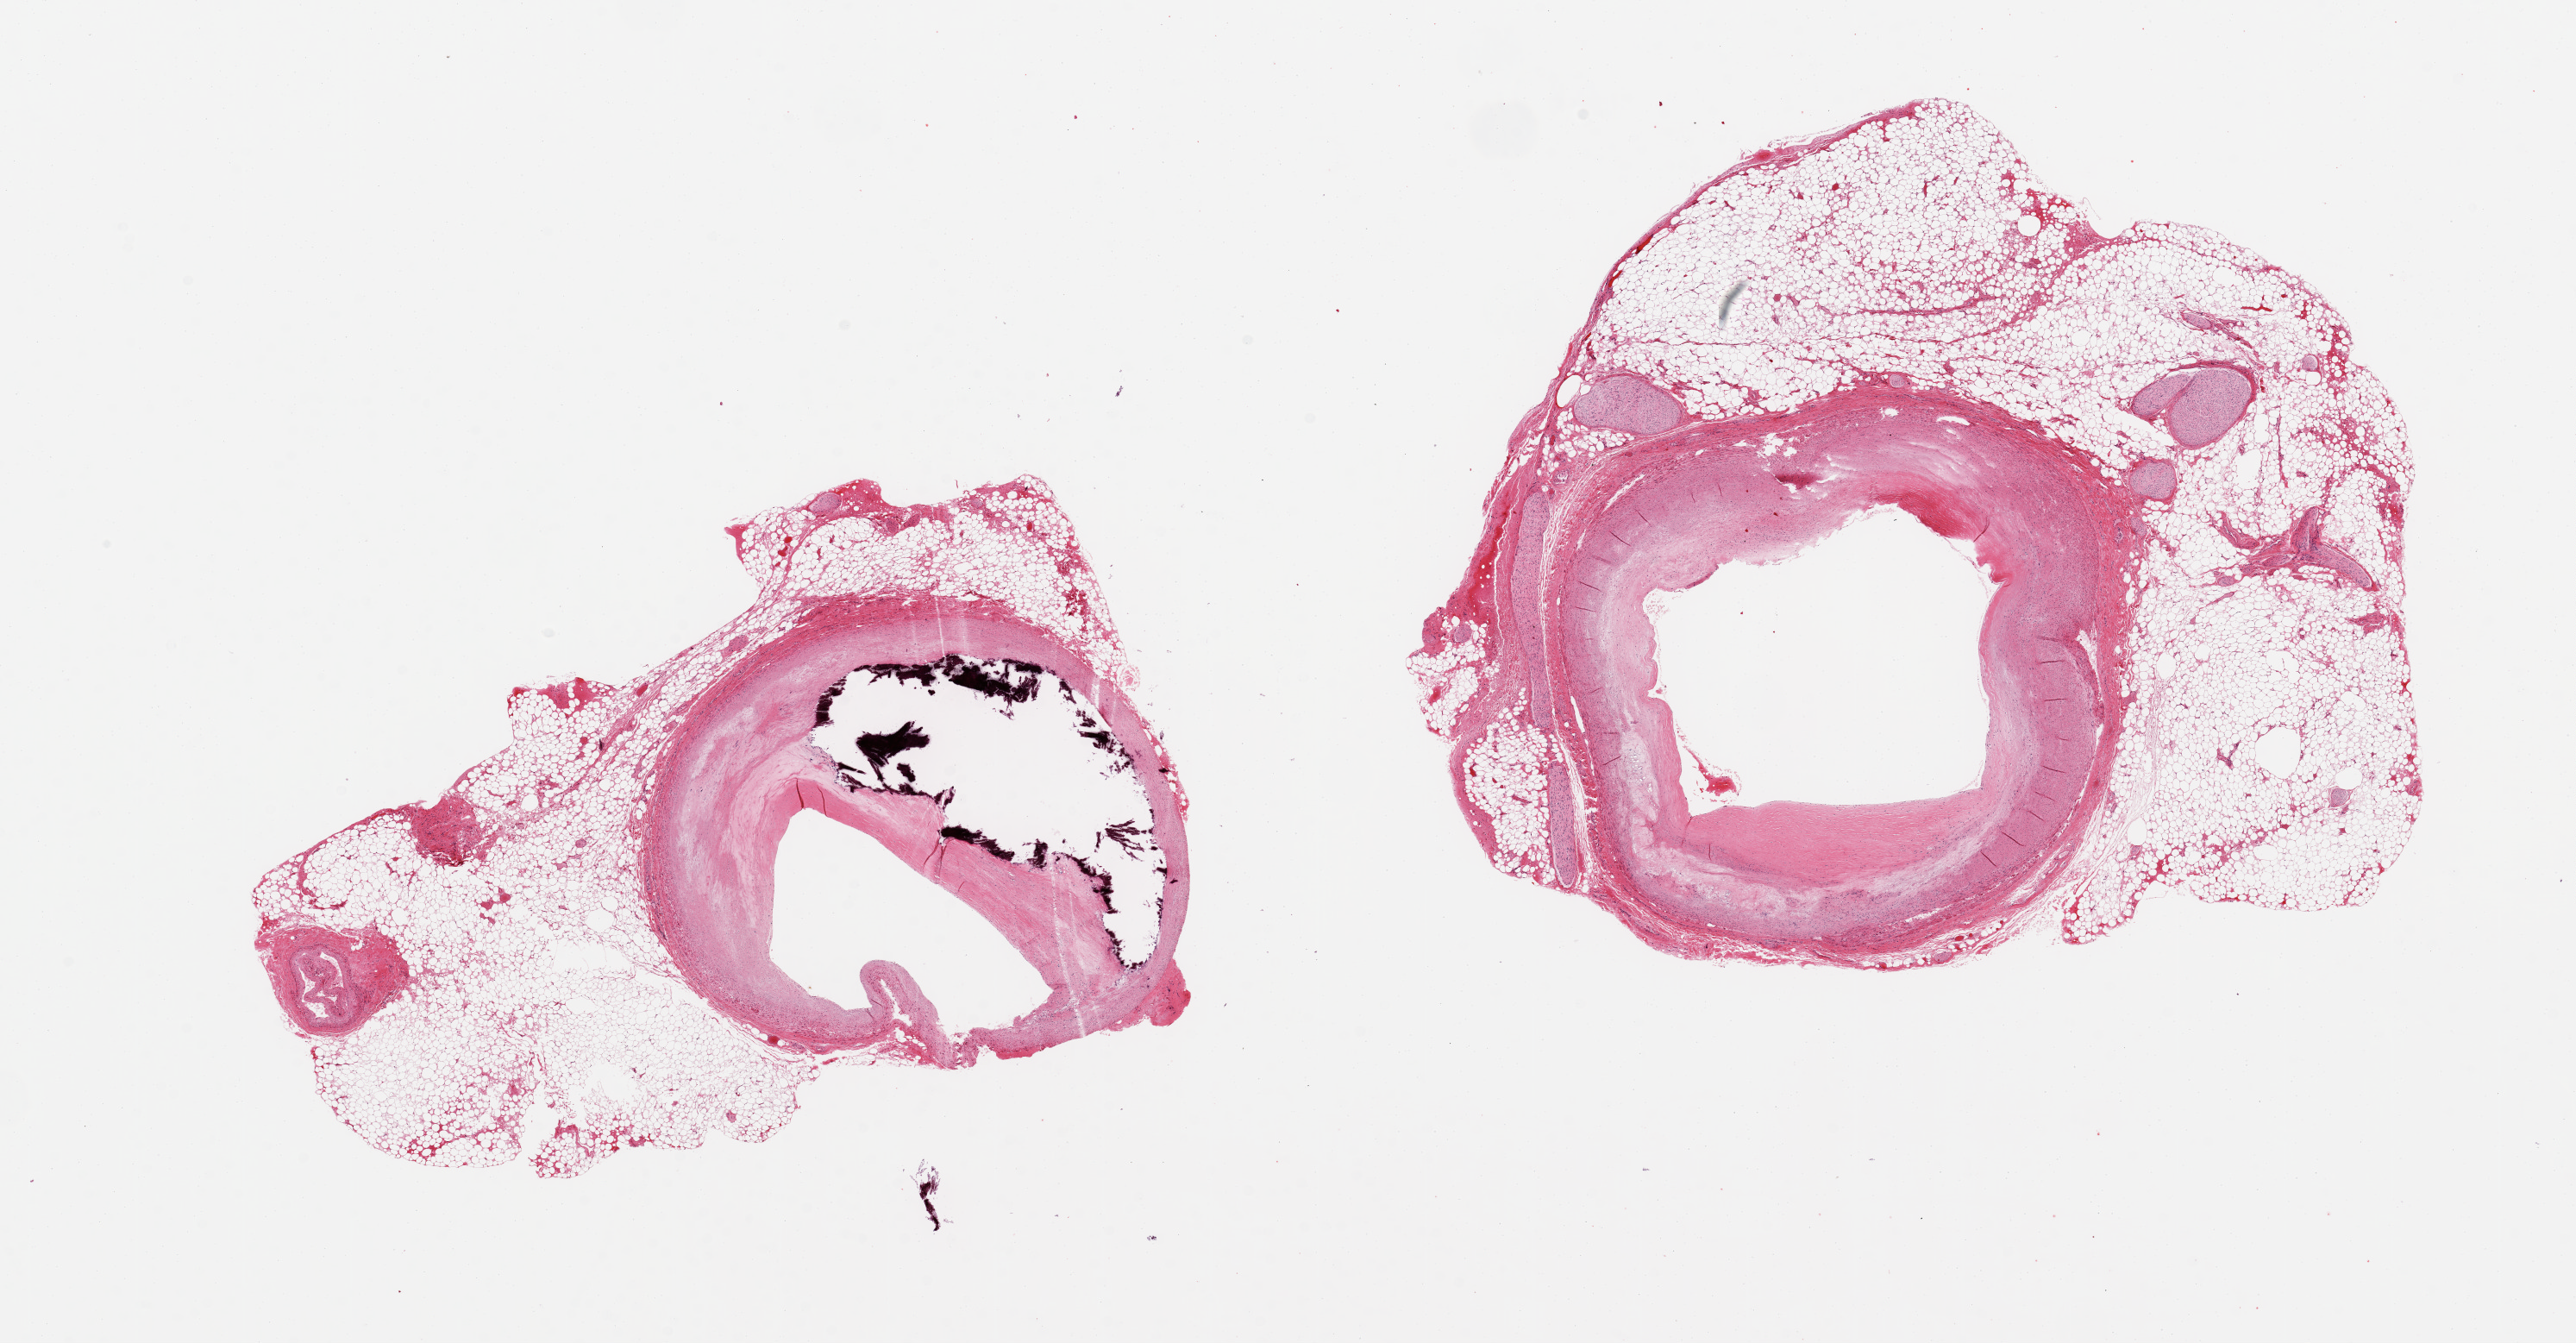
Digitized haematoxylin and eosin-stained section, brightfield, whole scanned area (about 23.6 x 12.3 mm, from a 20x scan) shown as a low-resolution overview, PAXgene-fixed, paraffin-embedded tissue, target tissue: coronary artery, tissue donor sample. Donor sex: male.
• reviewer comment on this tissue sample: 2 pieces ~ 5 mm diameter; 1 with 50% calcified plaque; each has ~50% adipose tissue